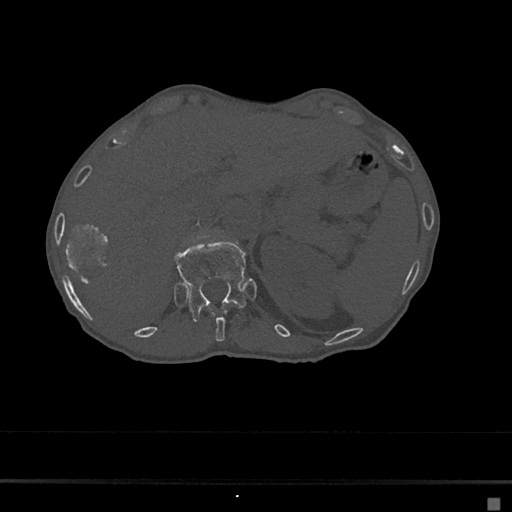
CT including the spine, one axial slice. Slice 134 of 797 in the series (ordered by position). Reconstruction kernel Br40s/3. 120 kVp. Bone window (W 1800 / L 400 HU). 0.5 mm slice thickness. 512 × 512 image matrix, field of view 360 × 360 mm. Patient: female, 68 years. From the clinical record (not read from this slice): primary cancer: renal.
Structures marked on this image (semi-automatic segmentation, software-assisted and operator-edited):
- T11 vertebra: bounding box <211,310,229,342> (left, top, right, bottom; pixels)
- T12 vertebra: <174,239,247,321>